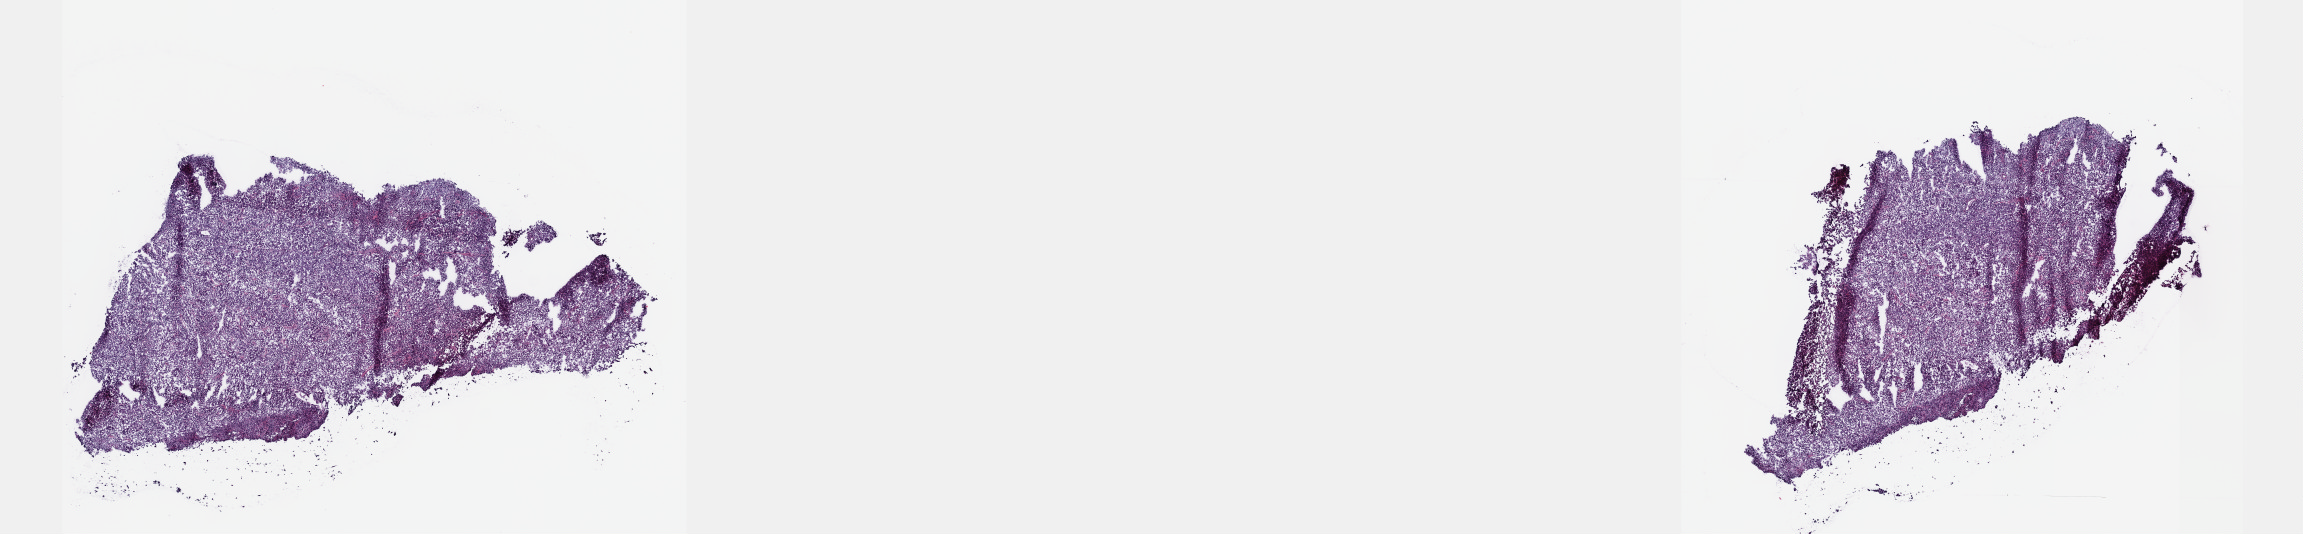
H&E whole-slide image — low-resolution overview of the scanned area, about 18.6 x 4.3 mm (from a 40x scan). Frozen section from the top of the tissue portion. Metastatic tumour sample, sampled site not recorded. Male, age 64 years at initial diagnosis. Composition of this section per pathologist review: tumour cells 85%, tumour nuclei 85%, normal cells 0%, stromal cells 15%, necrosis 0%. Inflammatory infiltration, as recorded: lymphocyte infiltration 3%, monocyte infiltration 1%, neutrophil infiltration 1%.
- this section: metastatic tumour tissue
- patient diagnosis: Malignant melanoma, NOS